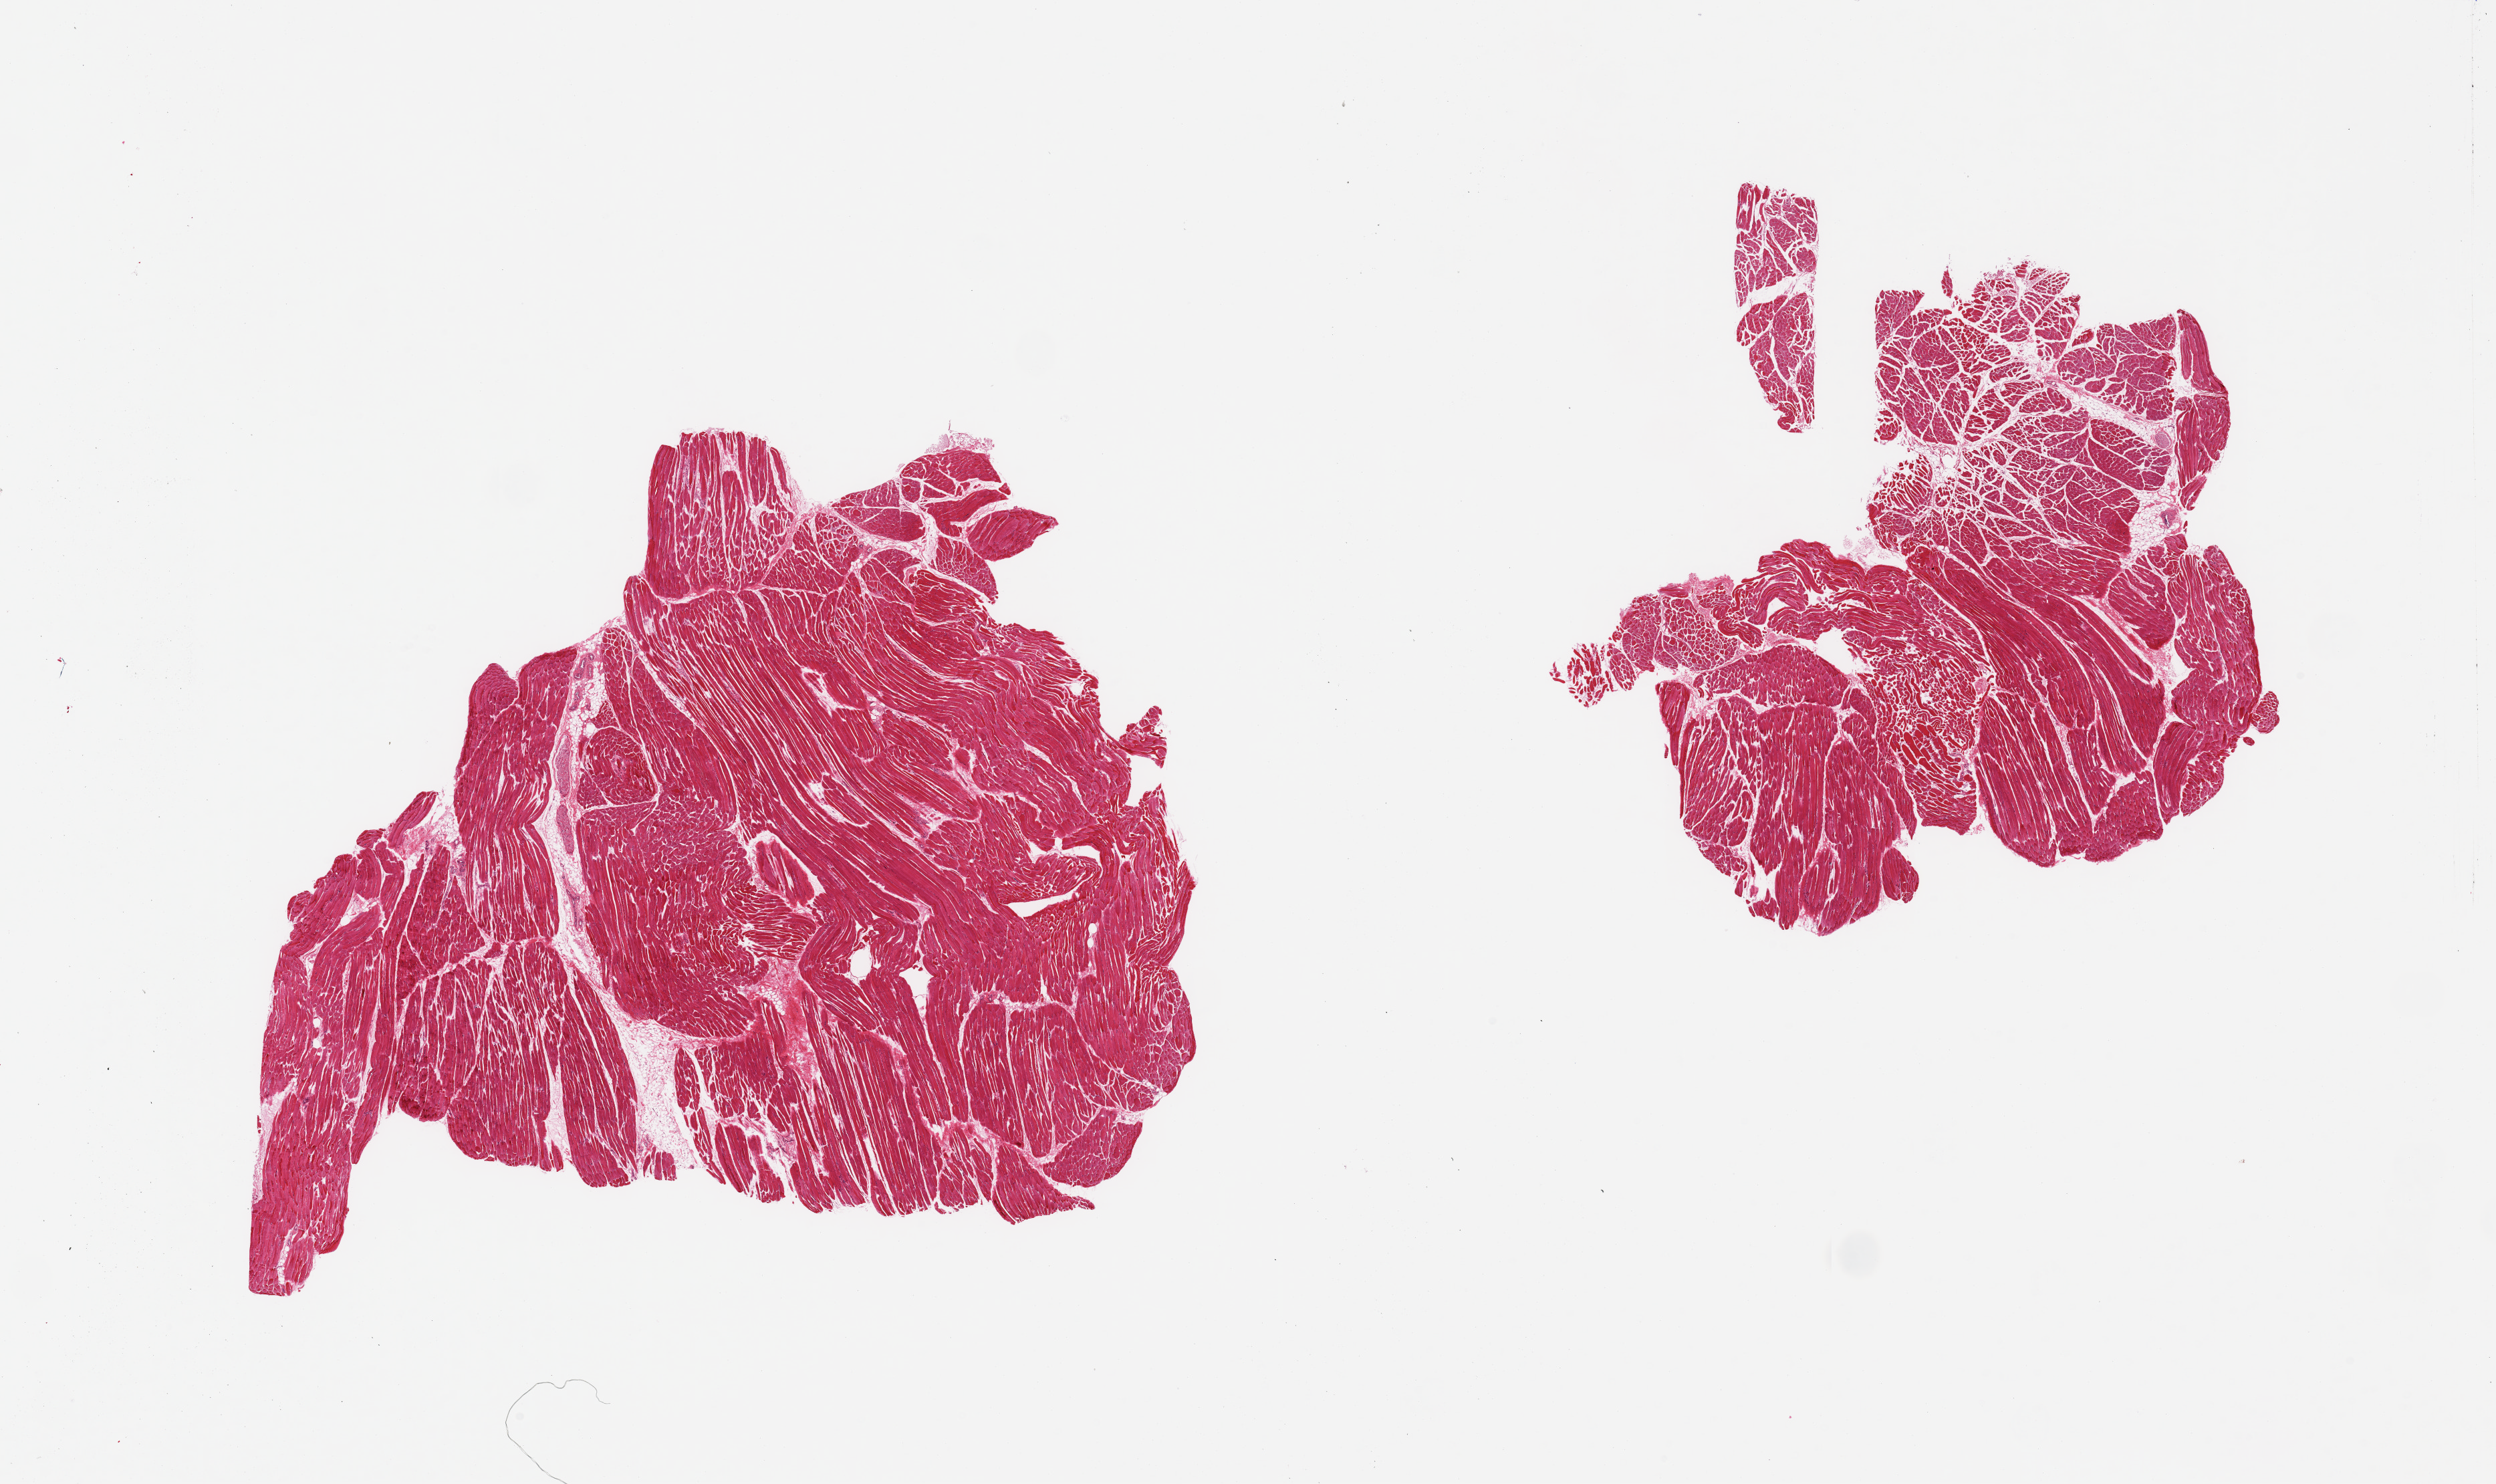
H&E whole-slide image, brightfield, shown as a low-resolution overview of the whole scanned area (about 29.5 x 17.6 mm, acquisition: 20x scan), PAXgene-fixed paraffin-embedded (PFPE) section, section of skeletal muscle (target tissue), donor tissue sample. Donor sex: male.
Review note (as recorded): 2 pieces; ~5% of moderately autolyzed internal fat.